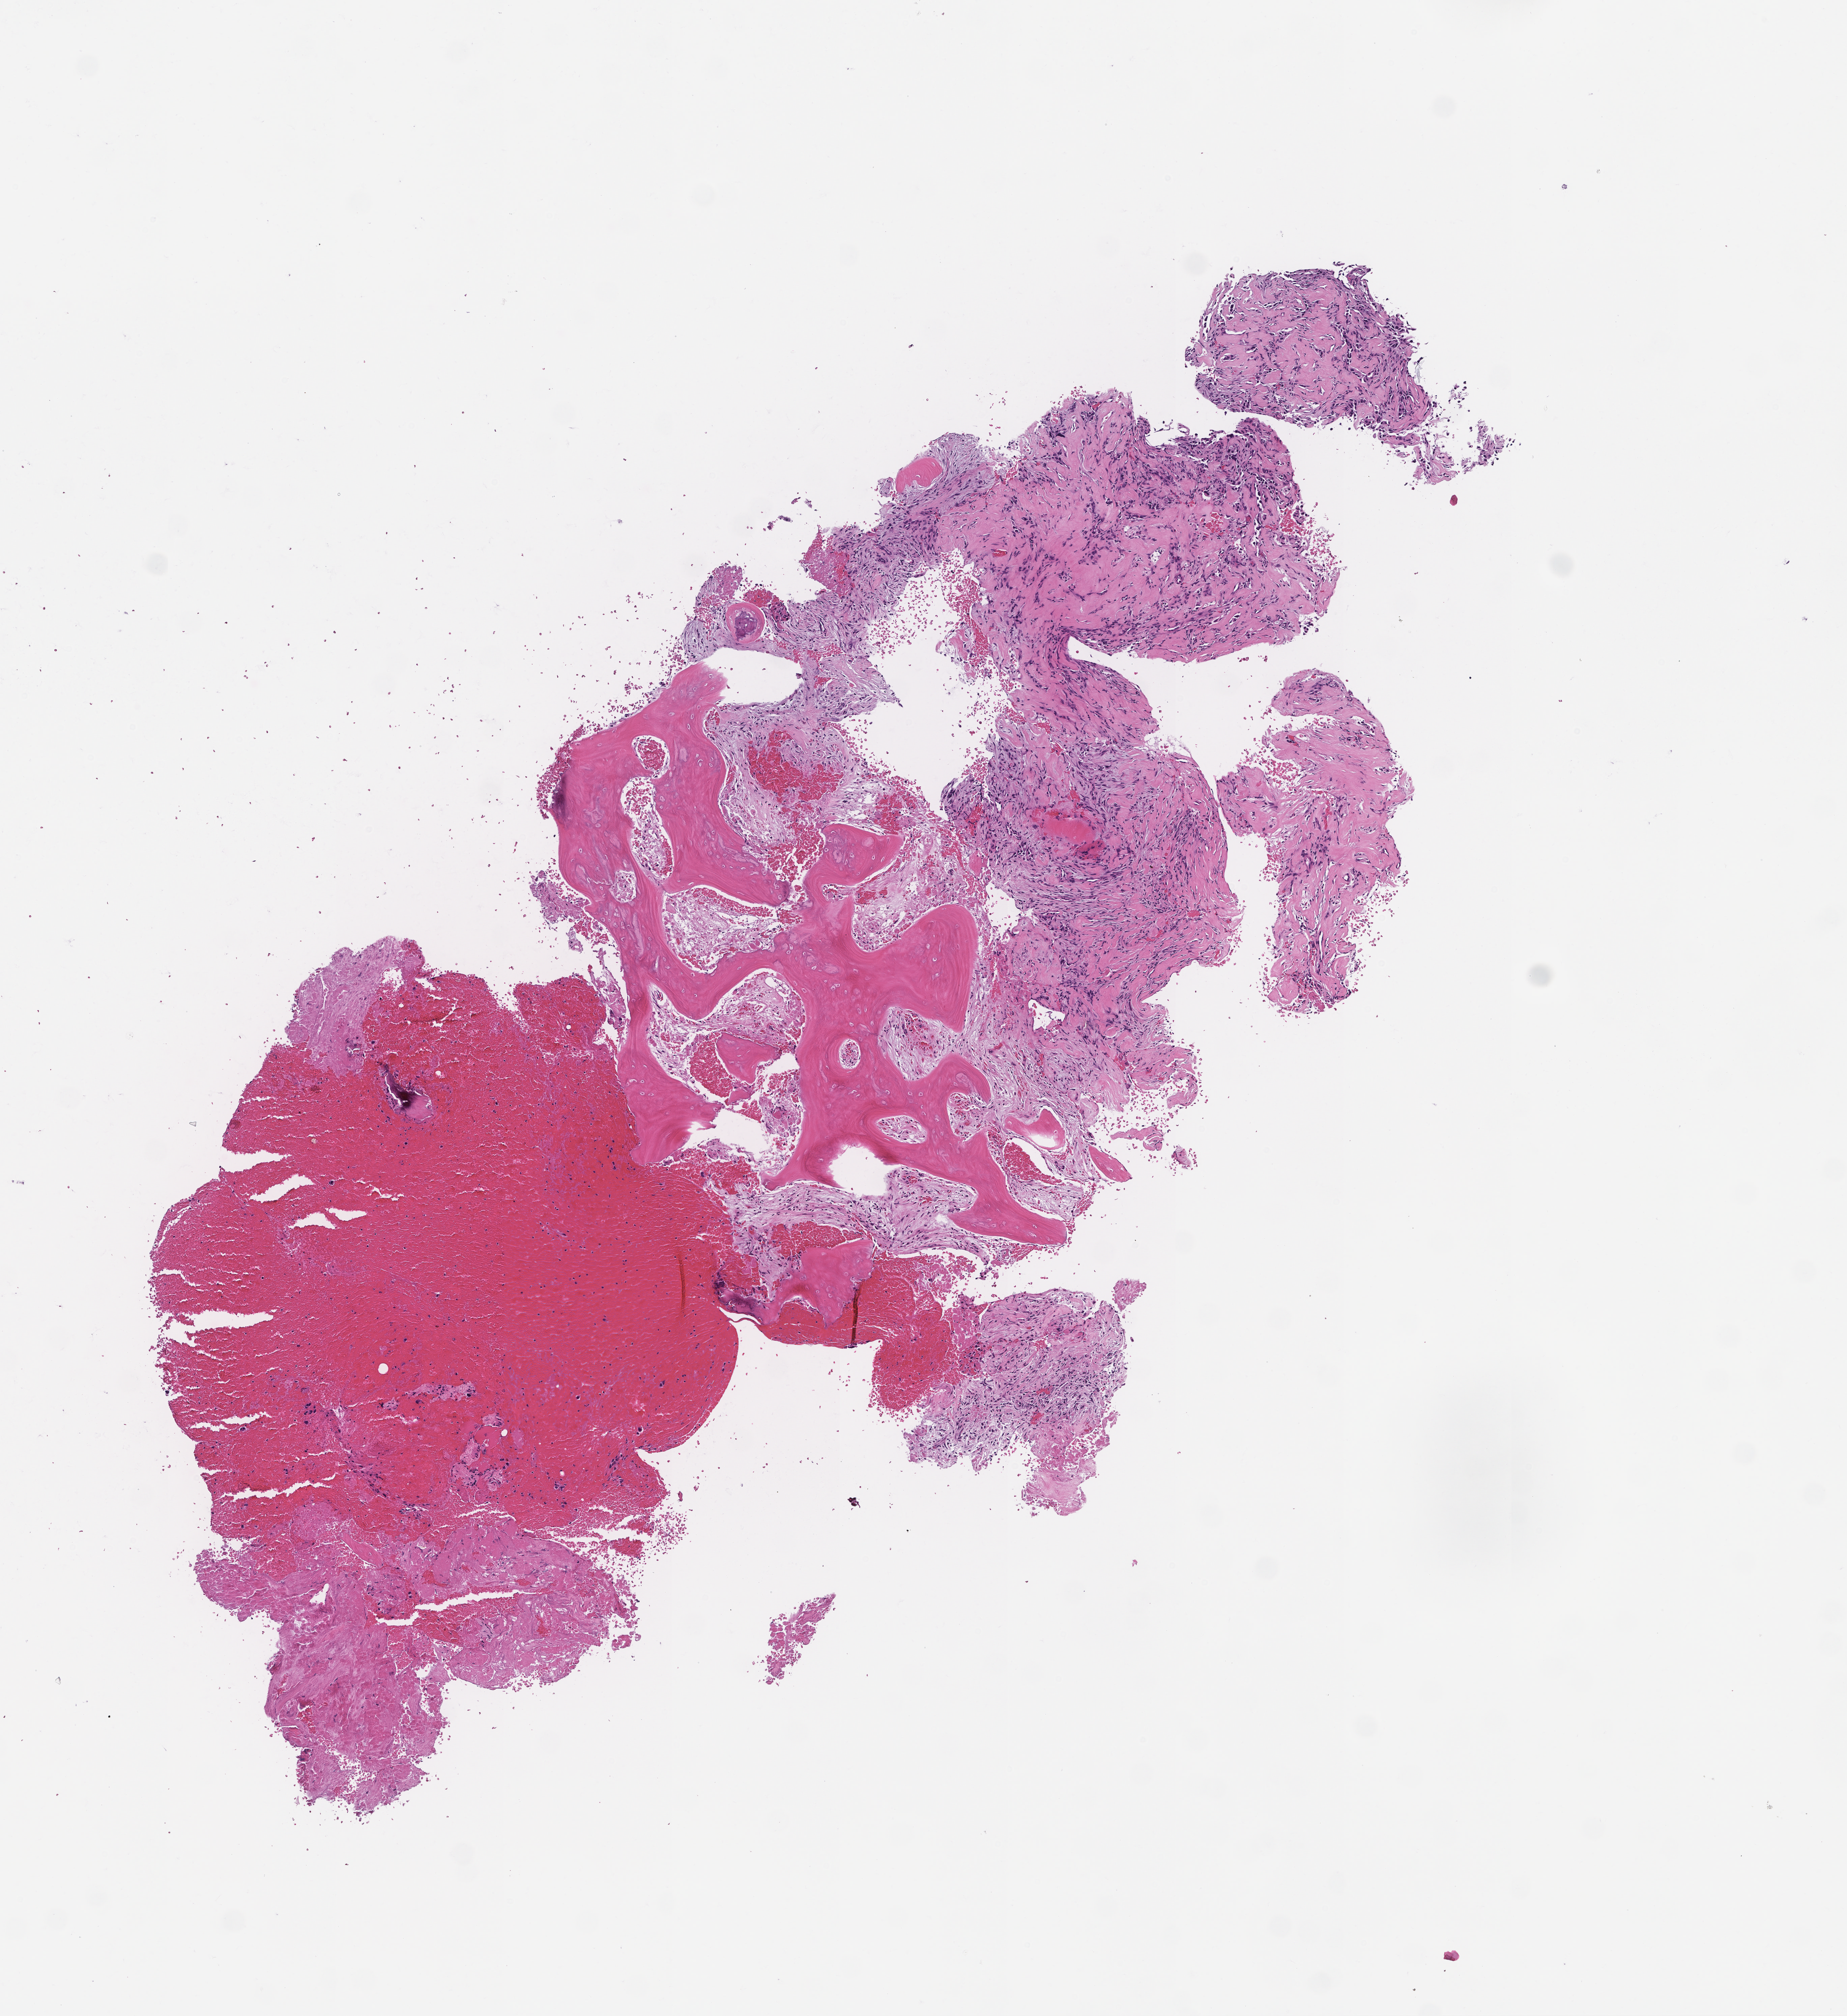
Haematoxylin and eosin whole-slide image — whole scanned area (about 5.5 x 6.0 mm) shown as a low-resolution overview; formalin-fixed paraffin-embedded section. Patient sex: male.
This section: metastasis (sampled organ not recorded). Primary diagnosis of the patient: Invasive Breast Carcinoma.